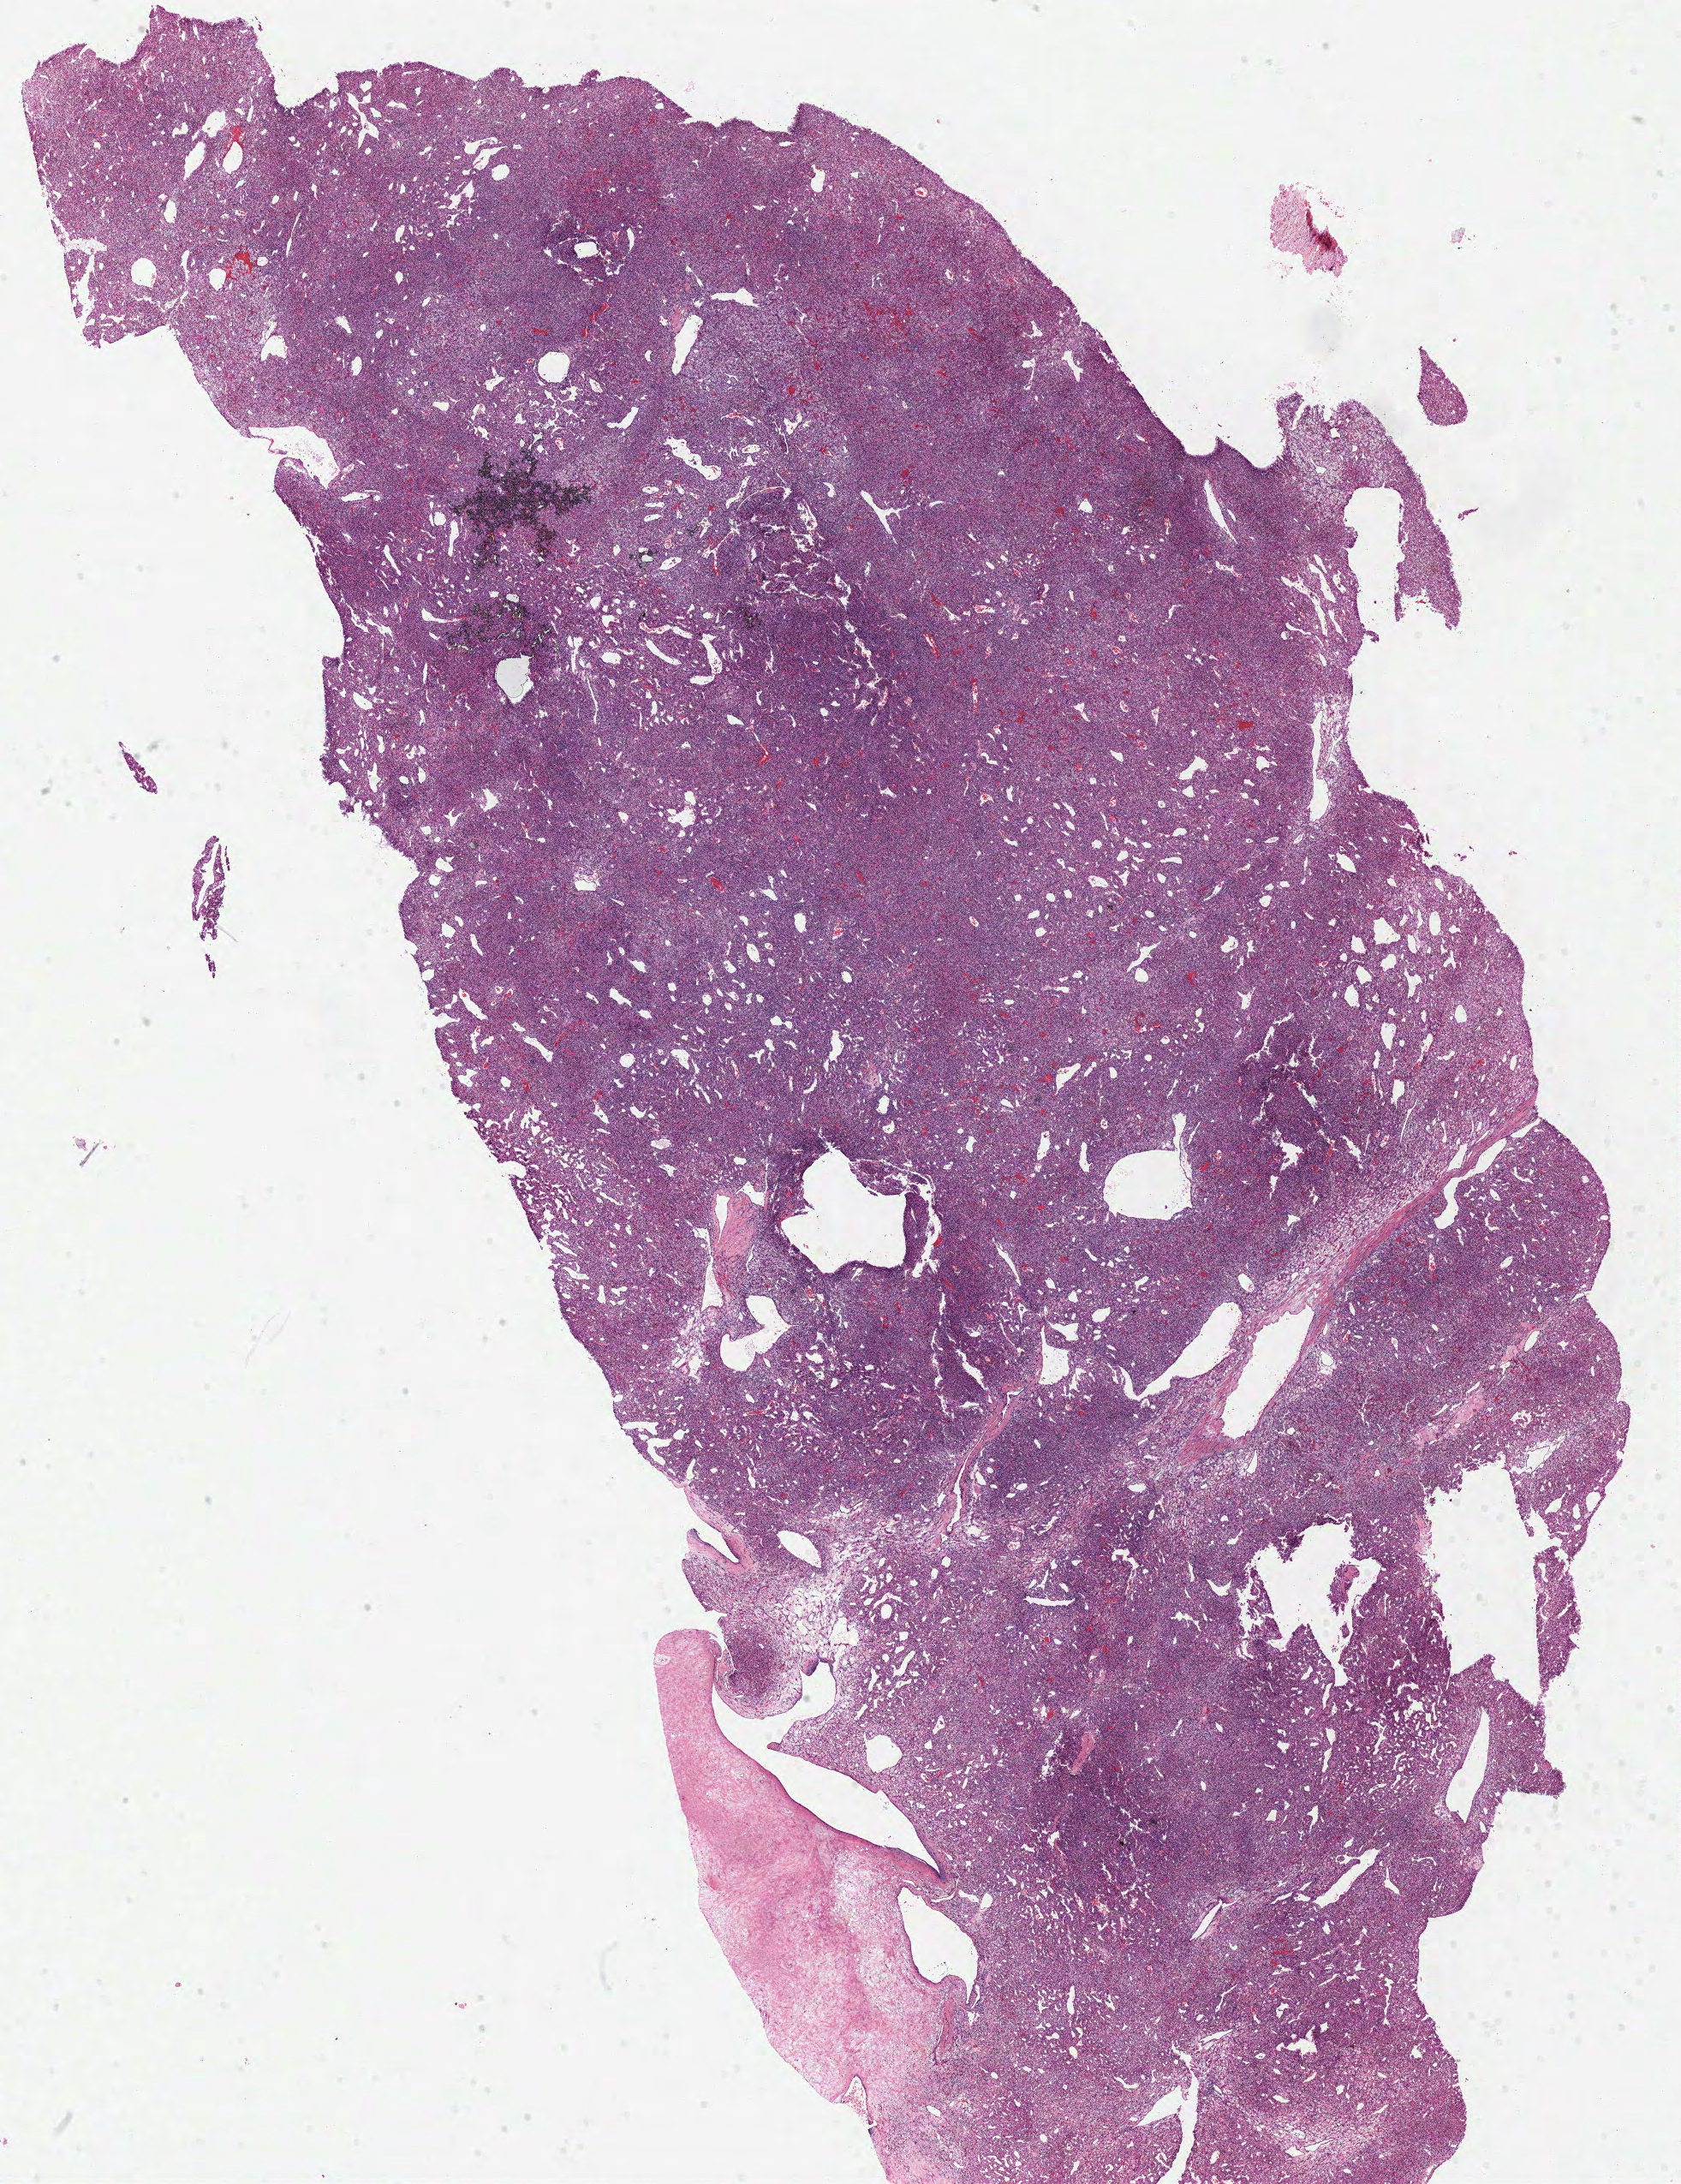
Digitized H&E tissue section (whole slide), a low-resolution overview of the entire scanned area, about 15.5 x 20.1 mm, formalin-fixed paraffin-embedded (FFPE) diagnostic section, primary tumour sample from the kidney. Female patient; age at initial diagnosis 51 years. Histologic grade: G2 (moderately differentiated).
- TNM: T3a N0 M0
- diagnosis: Clear cell adenocarcinoma, NOS
- AJCC pathologic stage: III